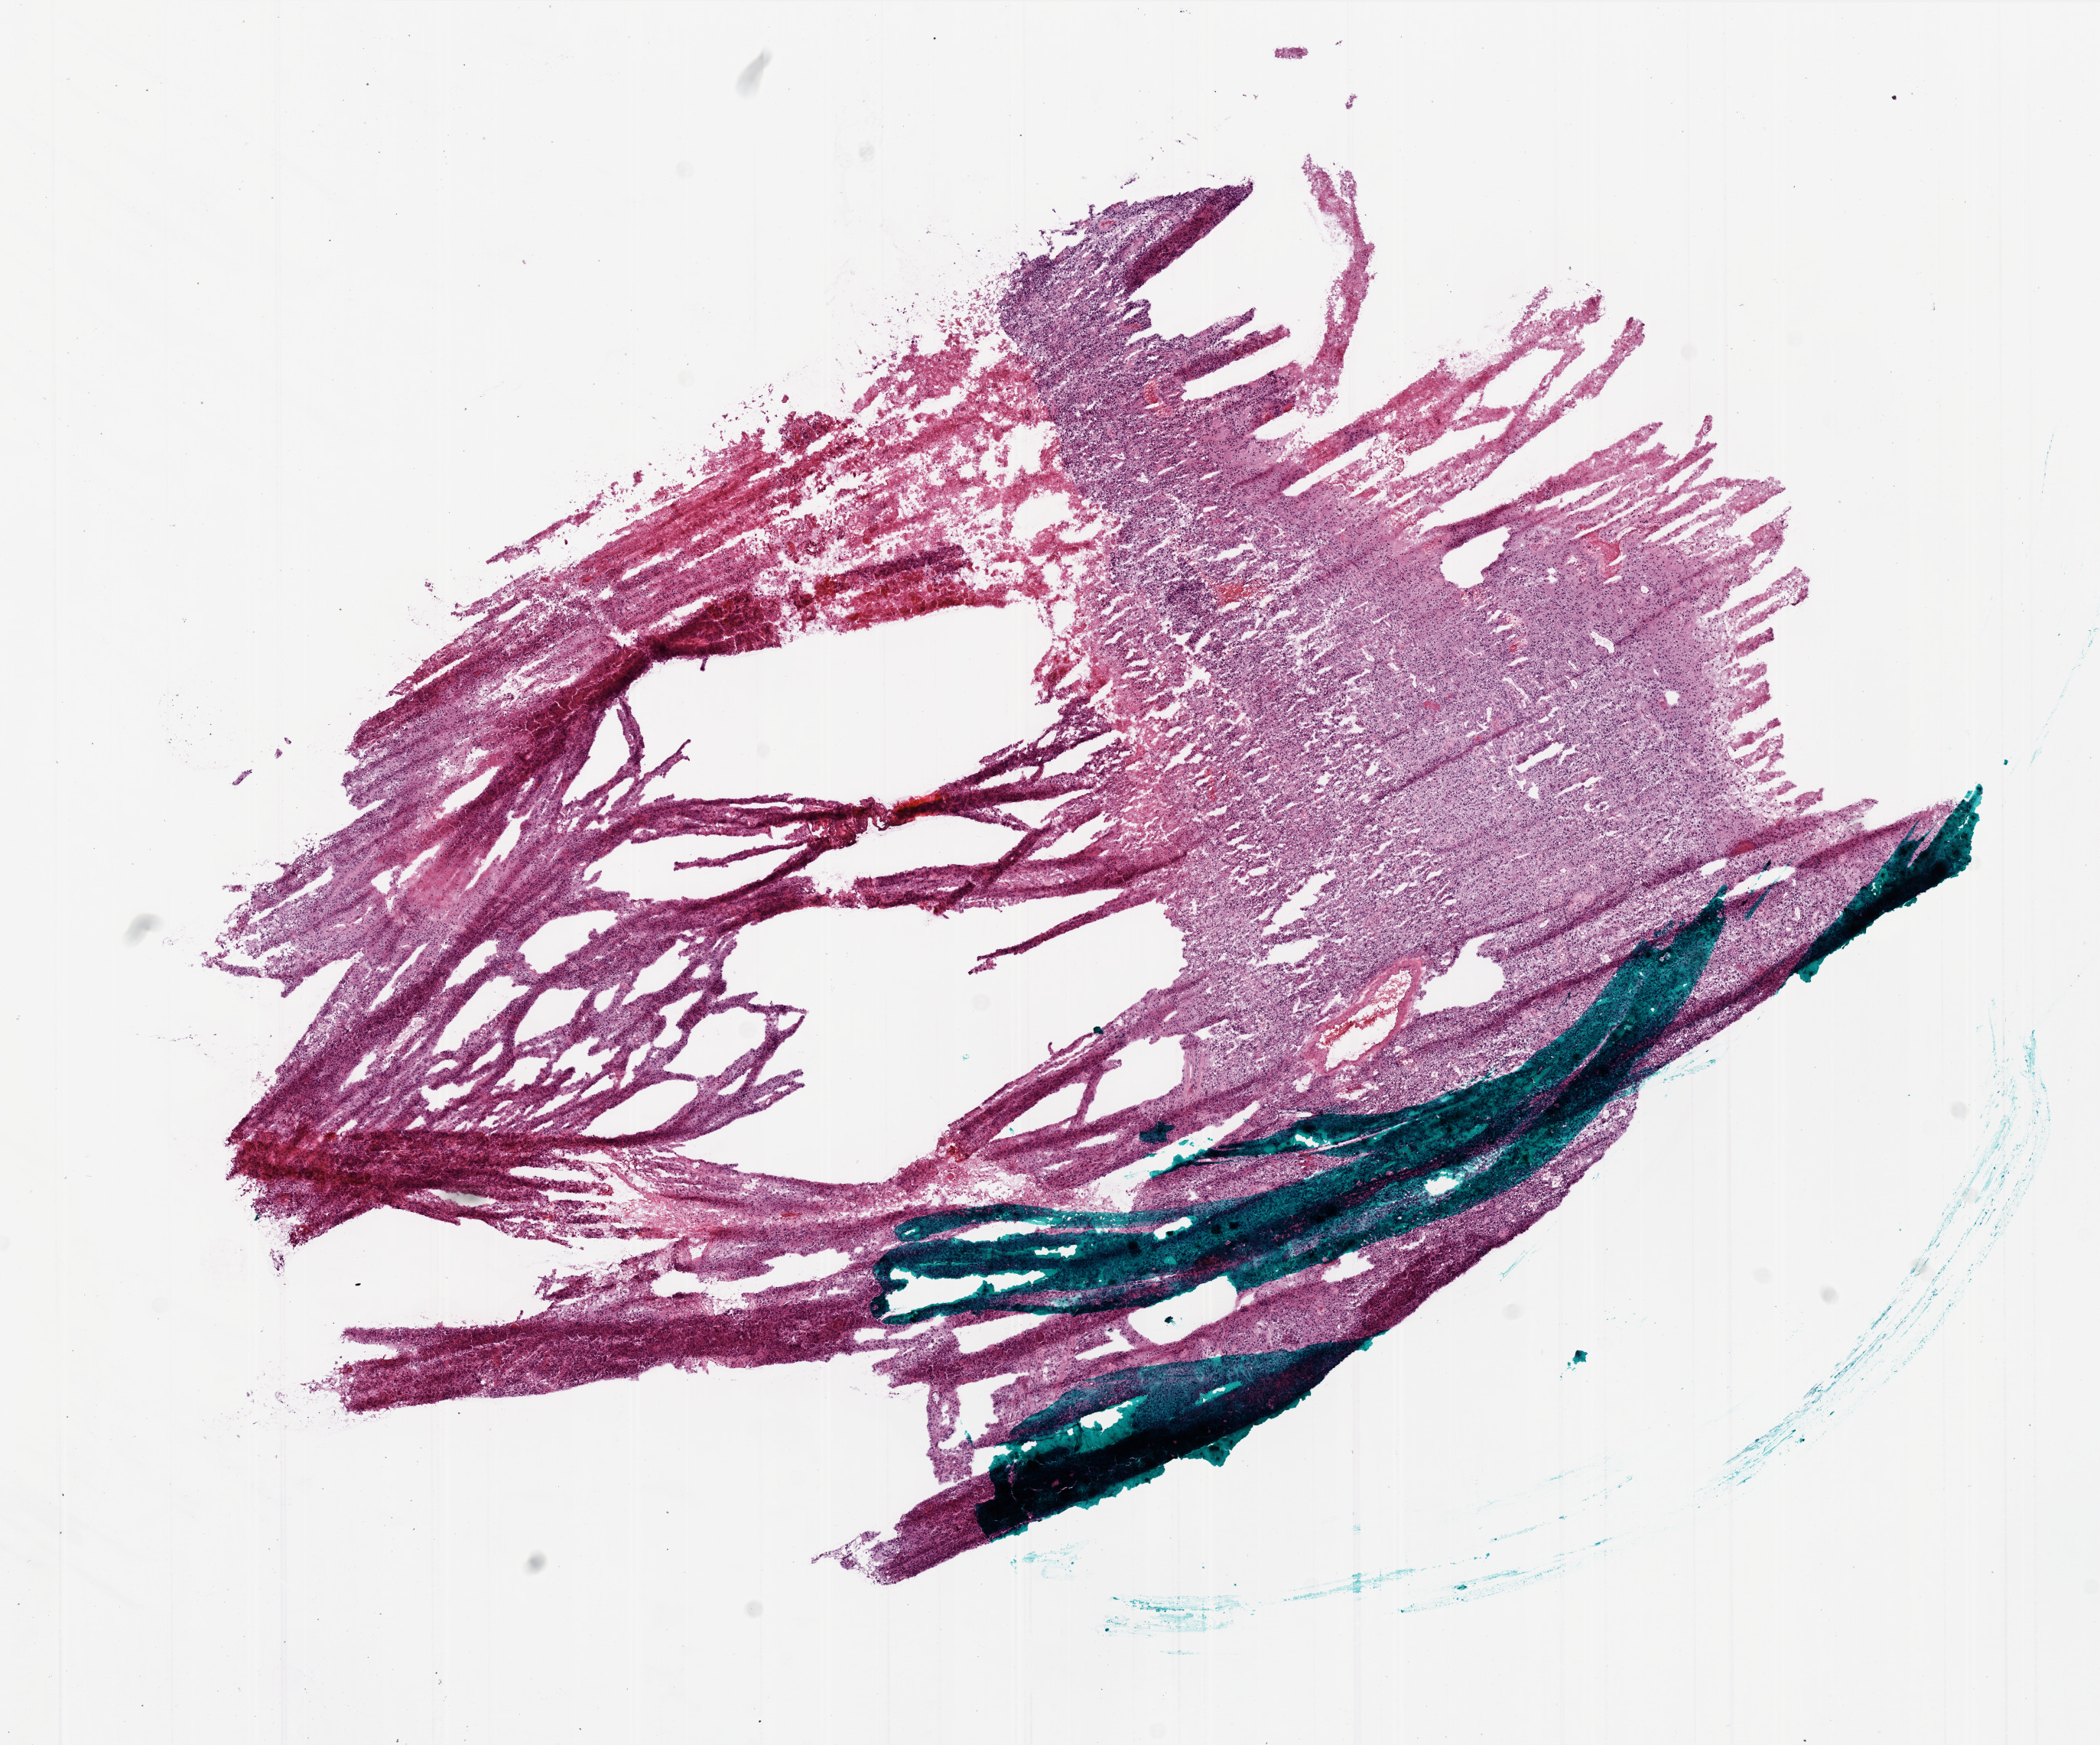
Digitized H&E tissue section (whole slide), a low-resolution overview of the entire scanned area, about 11.0 x 9.1 mm (acquisition: 20x scan), frozen section from the bottom of the tissue portion, primary tumour sample from the brain. Female, age 69 years at initial diagnosis. Pathologist review of this section (percent, as recorded): tumour cells 75%, tumour nuclei 100%, normal cells 0%, stromal cells 0%, necrosis 25%.
Histologic diagnosis: Glioblastoma.